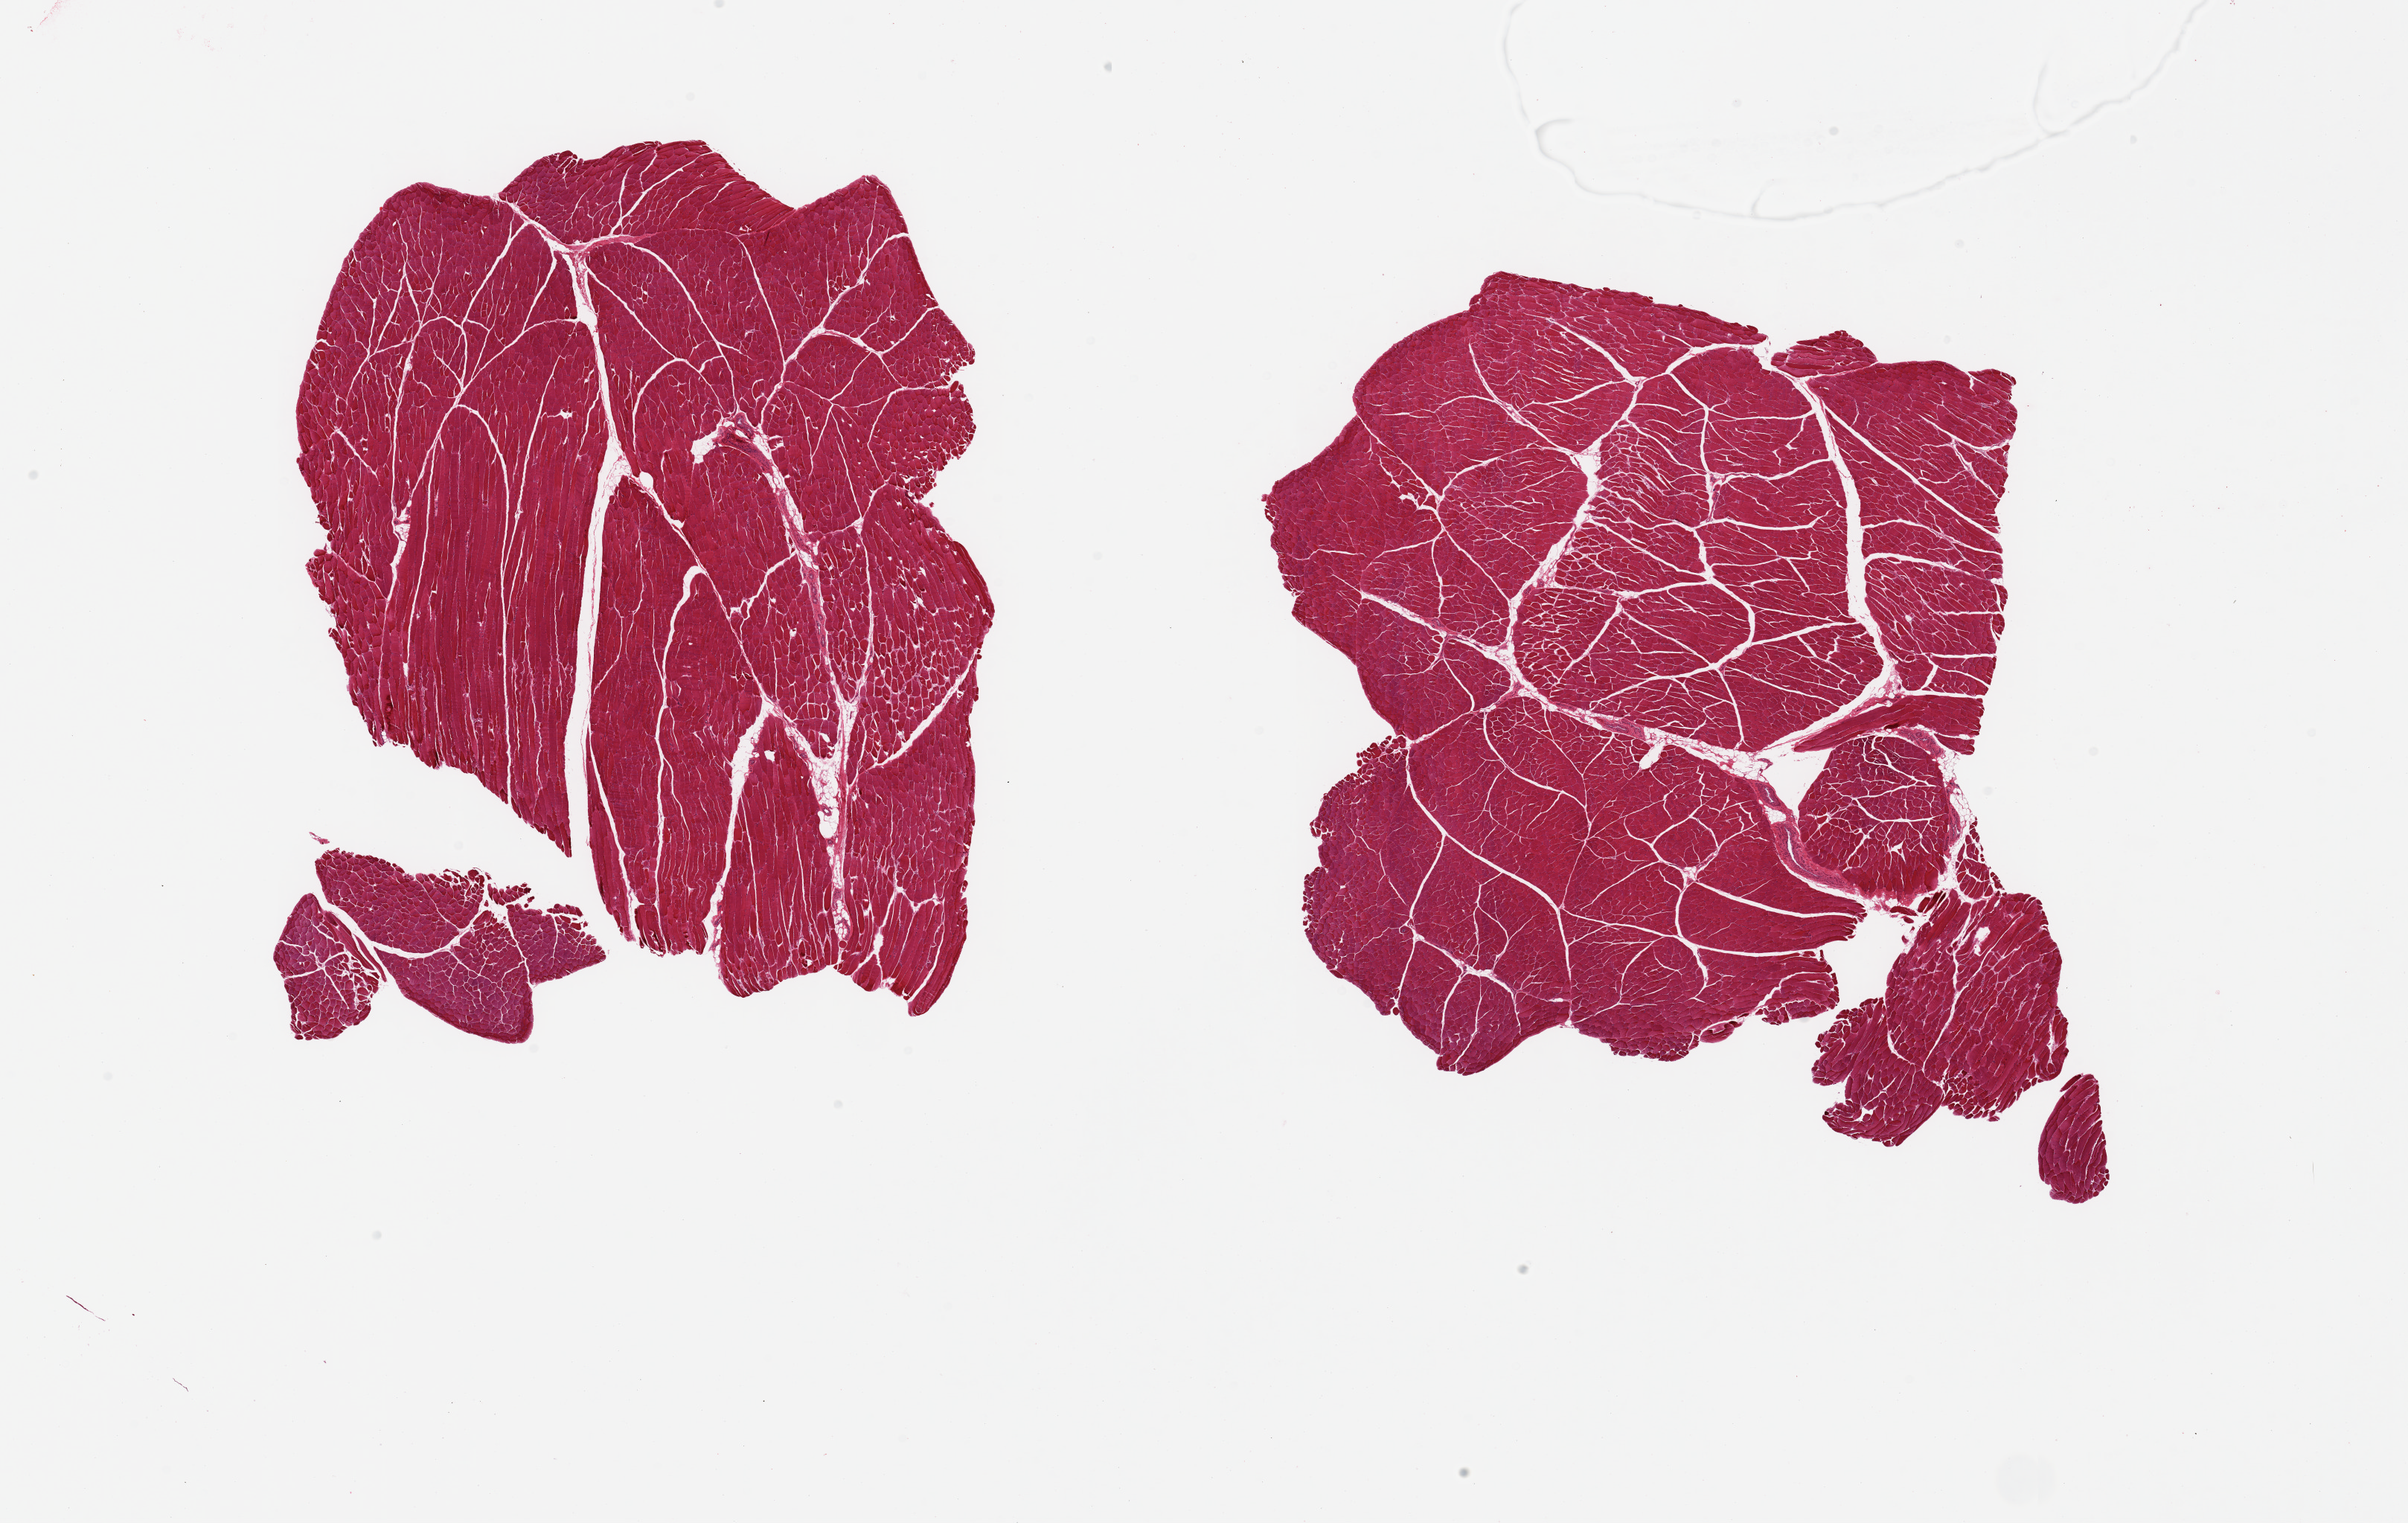
Digitized hematoxylin and eosin (H&E)-stained section — a low-resolution overview of the entire scanned area, about 25.6 x 16.2 mm. PAXgene-fixed paraffin-embedded (PFPE) section. Sampled site (target tissue): skeletal muscle. Donor tissue sample.
Pathologist's review note for this sample: 2 pieces.